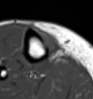
MRI of an extremity soft-tissue mass, one axial slice; slice 16 of 54 in the series (ordered by position); MR volume resampled by the dataset authors to the PET/CT grid (not the native acquisition matrix); 3.27 mm slice thickness; 93 × 99 image matrix. Female patient. Case-level facts recorded for this patient, not image findings: histological type: undifferentiated – high grade; grade: high; site of the primary tumour: right thigh.
Annotated regions visible in this slice (expert contour drawn on MRI and transferred to this co-registered scan by the dataset authors):
- gross tumour volume (mass): bounding box (x1, y1, x2, y2) in pixels: (36, 29, 60, 55)